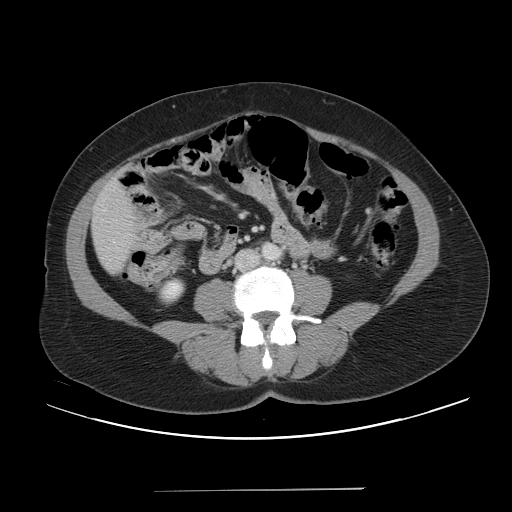
Contrast-enhanced abdominal CT, one axial slice; slice 6 of 56 in the series (ordered by position); 120 kVp; intravenous contrast given; soft-tissue window (W 400 / L 40 HU); 5 mm slice thickness; 512 × 512 image matrix, field of view 419 × 419 mm. Female patient, age 54 years. Case-level facts recorded for this patient, not image findings: diagnosis: colorectal cancer liver metastases, imaged before liver resection; multiple liver metastases: yes; largest metastasis: 3.2 cm; disease in both lobes: yes.
Outlined on this slice (expert manual segmentation):
- liver: bounding box (x1, y1, x2, y2) in pixels: (93, 180, 135, 273)